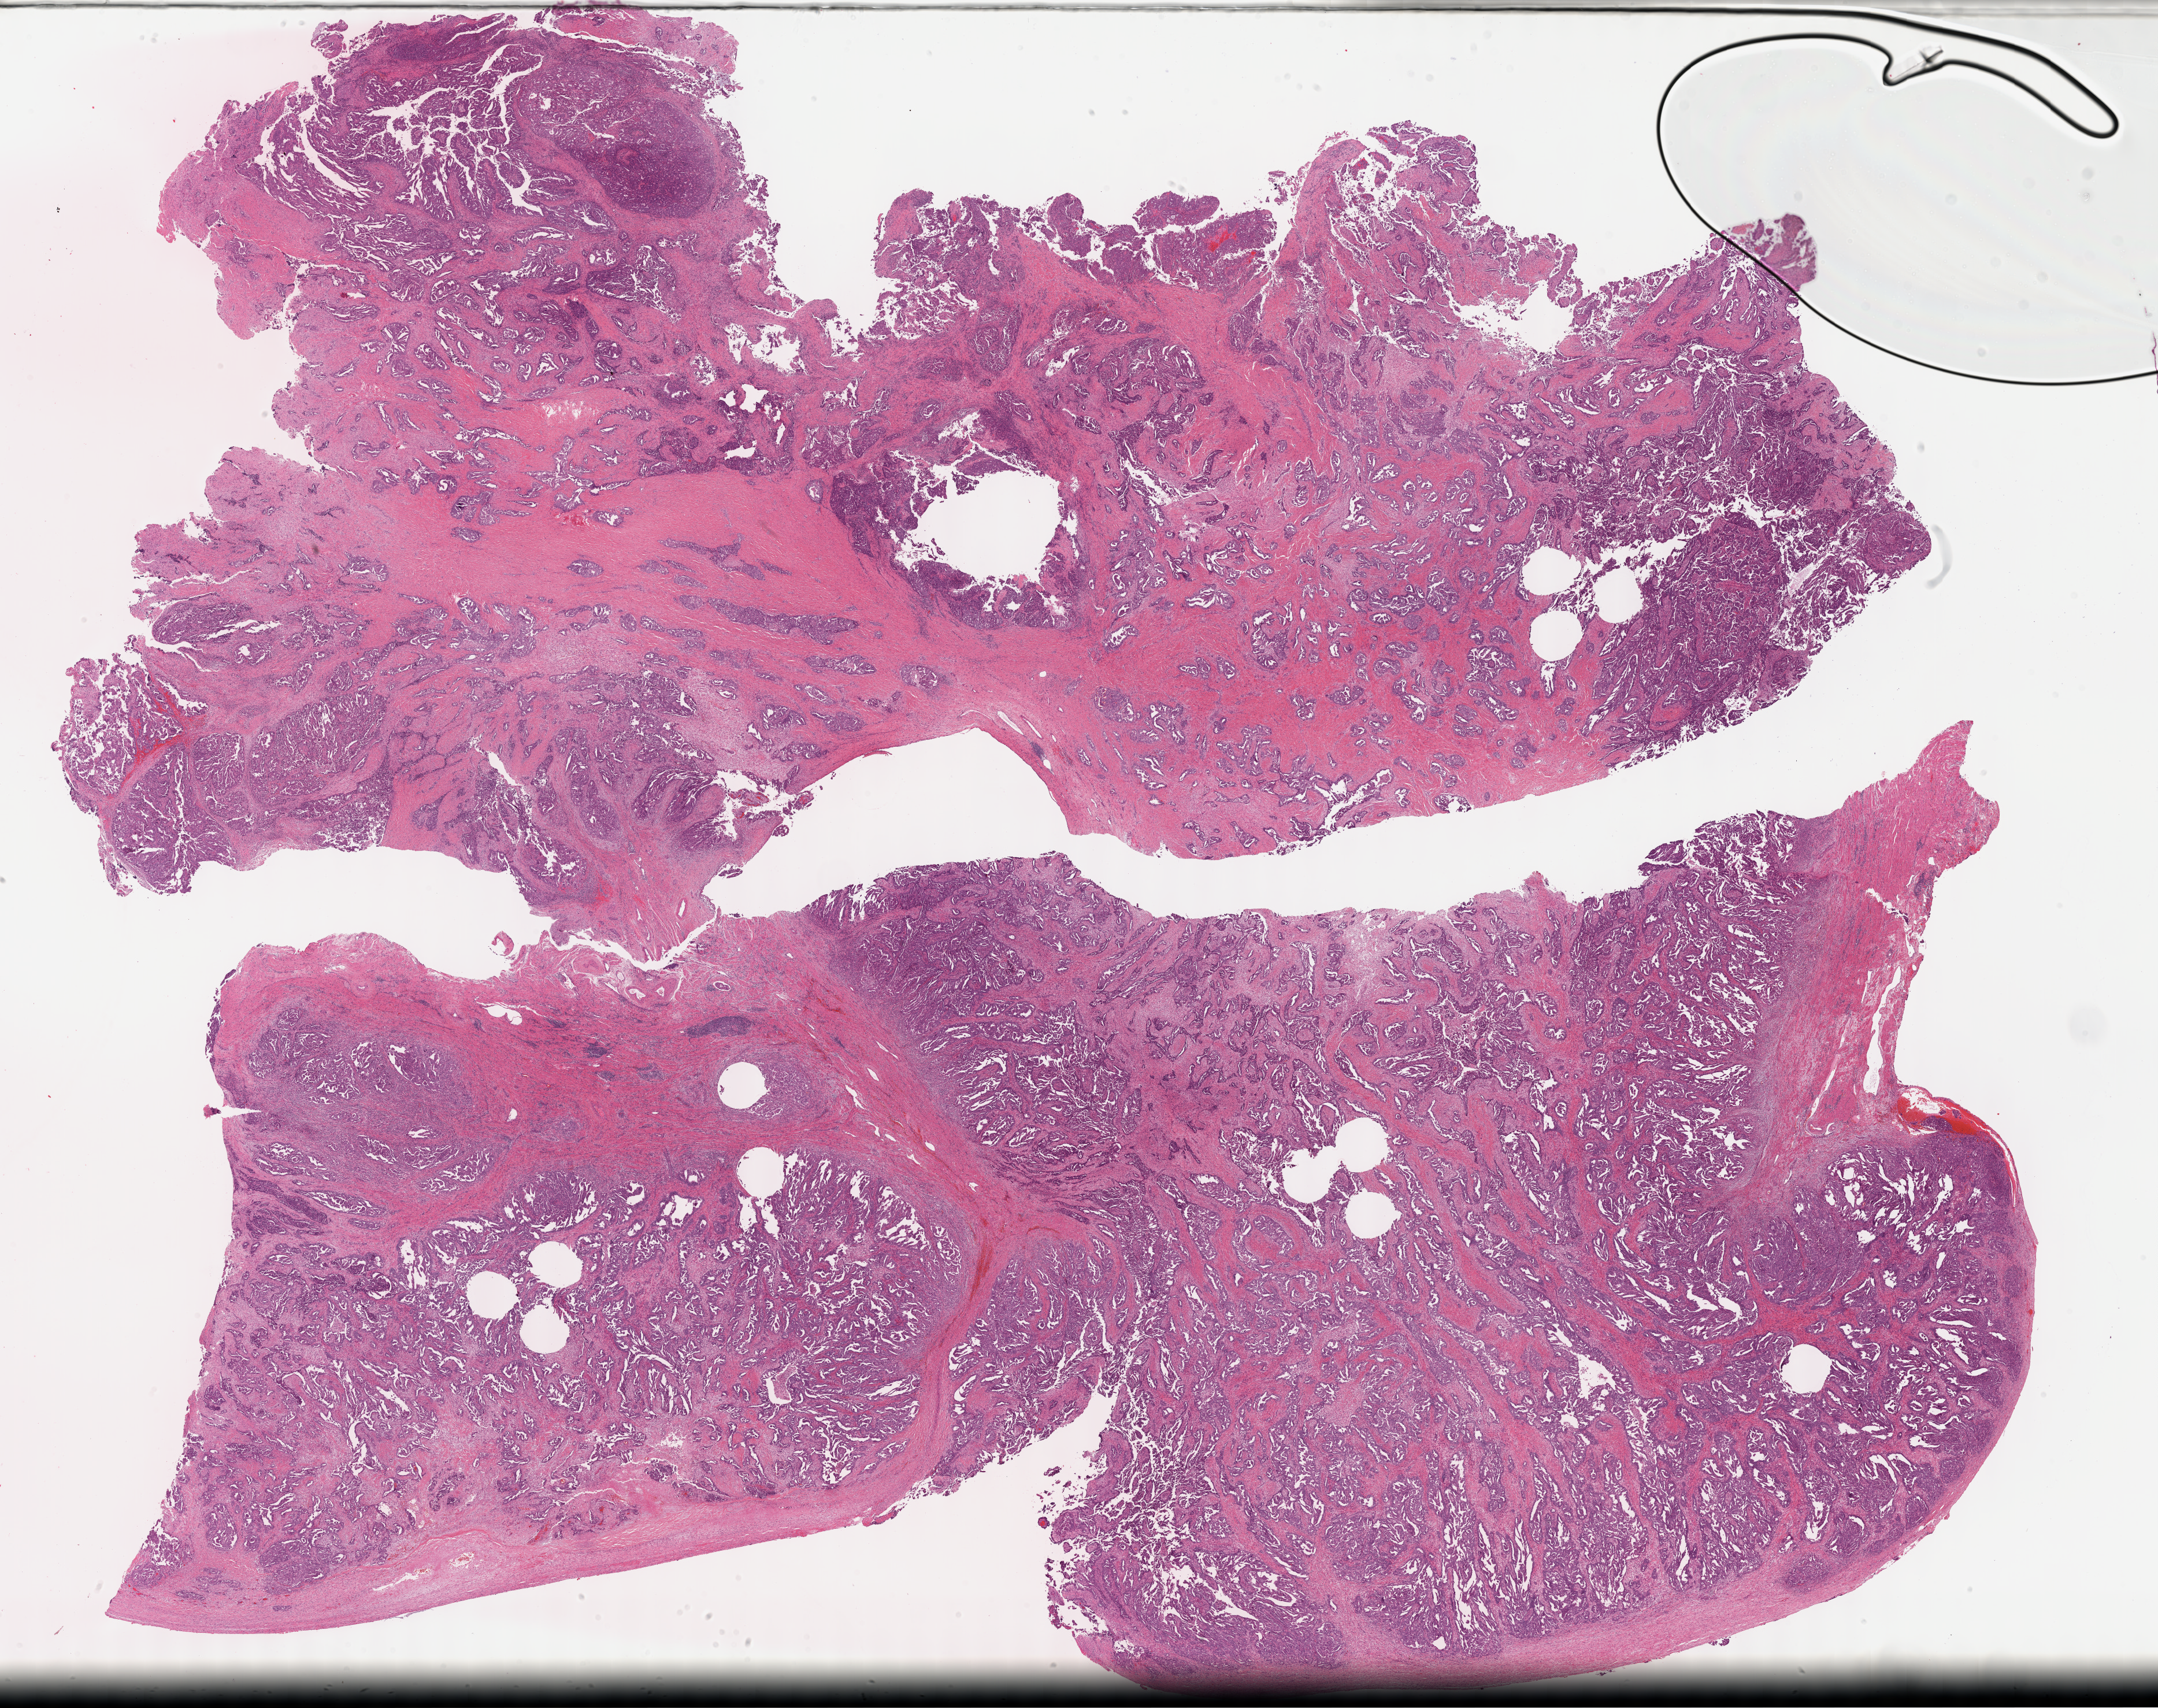
H&E whole-slide image, a low-resolution overview of the entire scanned area, about 30.2 x 23.9 mm; formalin-fixed paraffin-embedded (FFPE) diagnostic section; ovary, primary tumour sample. Patient: female, age at initial diagnosis 64 years. Histologic grade: G3 (poorly differentiated).
FIGO stage: IIIC. Laterality: left. Histologic diagnosis: Serous cystadenocarcinoma, NOS.